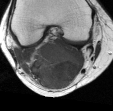
MRI of an extremity soft-tissue mass, one axial slice. Position 17 of 45 along the scan axis. MR volume resampled by the dataset authors to the PET/CT grid (not the native acquisition matrix). 3.27 mm slice thickness. 113 × 111 image matrix. Female patient. From the clinical record (not read from this slice): histological type: liposarcoma; site of the primary tumour: right thigh.
Annotated regions visible in this slice (expert contour drawn on MRI and transferred to this co-registered scan by the dataset authors):
- gross tumour volume (mass): bounding box (x1, y1, x2, y2) in pixels: (26, 42, 80, 88)